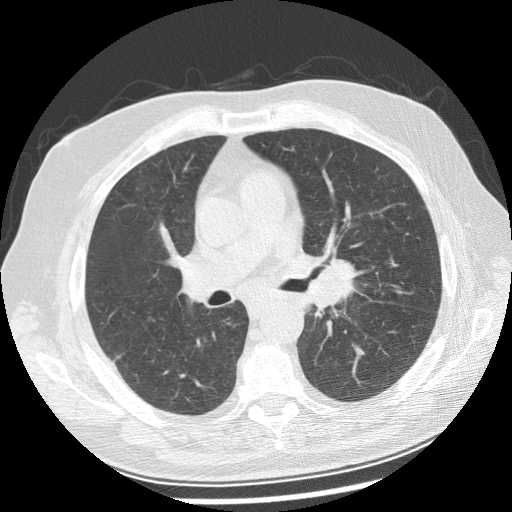
Low-dose screening chest CT, one axial slice. Position 144 of 250 along the scan axis. Reconstruction kernel STANDARD. 120 kVp. Lung window (W 1500 / L -600 HU). 2.5 mm slice thickness. 512 × 512 image matrix, field of view 360 × 360 mm.
Annotated regions visible in this slice (manually delineated by an expert):
- lesion 1 (tumor, left main bronchus): bounding box [x1, y1, x2, y2] px = [306, 260, 357, 309]